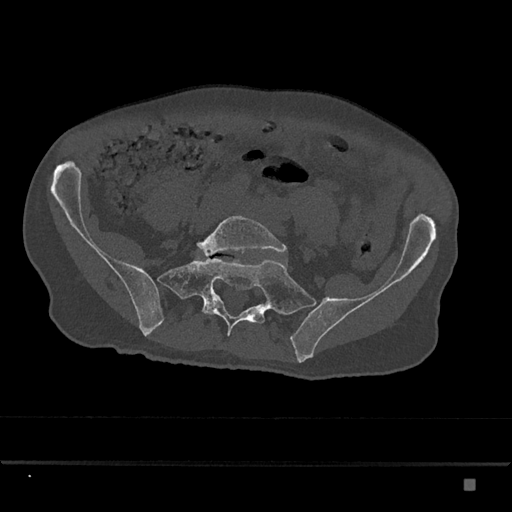
CT including the spine, one axial slice. Slice 235 of 797 in the series (ordered by position). 120 kVp. Bone window (W 1800 / L 400 HU). 0.5 mm slice thickness. 512 × 512 image matrix. Patient: male, 72 years. From the clinical record (not read from this slice): primary cancer: prostate.
Annotated regions visible in this slice (semi-automatic segmentation, software-assisted and operator-edited):
- L5 vertebra: bounding box <197,216,288,256> (left, top, right, bottom; pixels)